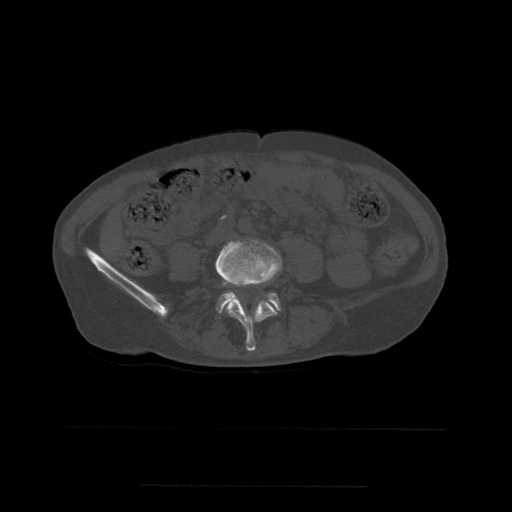
CT including the spine, one axial slice; slice 159 of 544 in the series (ordered by position); bone window (W 1800 / L 400 HU); 1.25 mm slice thickness; 512 × 512 image matrix. Patient age 58 years. Case-level facts recorded for this patient, not image findings: primary cancer: lung.
Structures marked on this image (semi-automatically segmented with operator editing):
- L4 vertebra: bounding box <216,241,282,351> (left, top, right, bottom; pixels)
- L5 vertebra: <217,278,281,313>